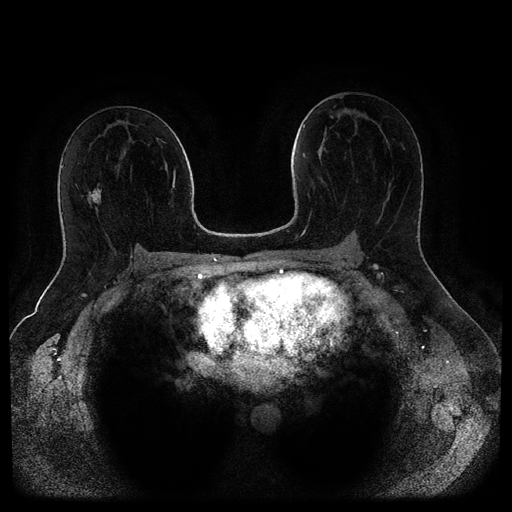
Breast MRI (dynamic contrast-enhanced, multi-phase), one axial slice. Position 53 of 116 along the scan axis. Dynamic contrast-enhanced series, time point 2 of 5 at this slice position (early post-contrast). 1.5 T. TE 2.6 ms, TR 5.3 ms. 512 × 512 image matrix, field of view 370 × 370 mm. Female patient, age 44 years.
Annotated regions visible in this slice (semi-automatically segmented with operator editing):
- breast lesion (labelled benign in the annotation): box from (x=89, y=186) to (x=102, y=204) px